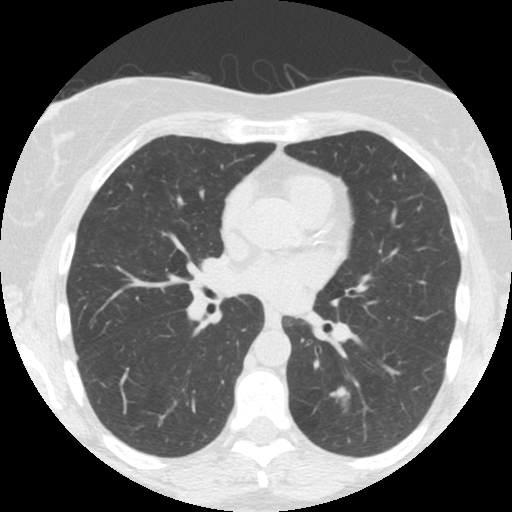
Low-dose screening chest CT, one axial slice; position 81 of 150 along the scan axis; reconstruction kernel STANDARD; lung window (W 1500 / L -600 HU); 512 × 512 image matrix, field of view 300 × 300 mm.
Structures marked on this image (outlined manually by an expert reader):
- lesion 1 (tumor, lower lobe of left lung): bounding box [x1, y1, x2, y2] px = [330, 388, 350, 403]